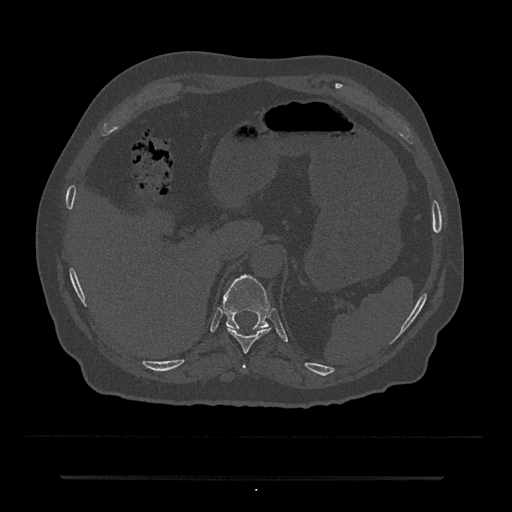
CT including the spine, one axial slice; slice 207 of 797 in the series (ordered by position); 120 kVp; bone window (W 1800 / L 400 HU); 0.5 mm slice thickness; 512 × 512 image matrix, field of view 437 × 437 mm. Patient: male, 69 years. From the clinical record (not read from this slice): primary cancer: prostate.
Annotated regions visible in this slice (semi-automatic segmentation, software-assisted and operator-edited):
- T10 vertebra: bounding box [x1, y1, x2, y2] px = [226, 327, 270, 353]
- T11 vertebra: [223, 275, 270, 330]
- T9 vertebra: [242, 364, 247, 370]